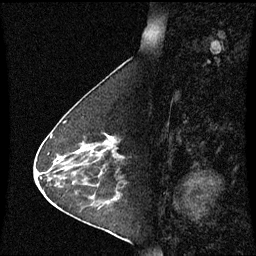
Breast MRI (dynamic contrast-enhanced), one sagittal slice. Dynamic contrast-enhanced series, image 2 of 3 at this slice position (ordered by acquisition). 1.5 T. TE 4.2 ms, TR 8.9 ms. 2 mm slice thickness. 256 × 256 image matrix, field of view 210 × 210 mm. Patient: female, 63 years. From the clinical record (not read from this slice): setting: breast cancer imaged before/during neoadjuvant chemotherapy; receptor status: HR-positive, HER2-negative.
Outlined on this slice (semi-automatic segmentation, software-assisted and operator-edited):
- analysis volume of interest (the breast-tissue region the enhancement analysis was run in; not a lesion): bounding box (x1, y1, x2, y2) in pixels: (76, 134, 124, 178)
- tumour enhancement mask (voxels above the 70 % enhancement threshold inside the analysis volume of interest): (106, 135, 115, 153)